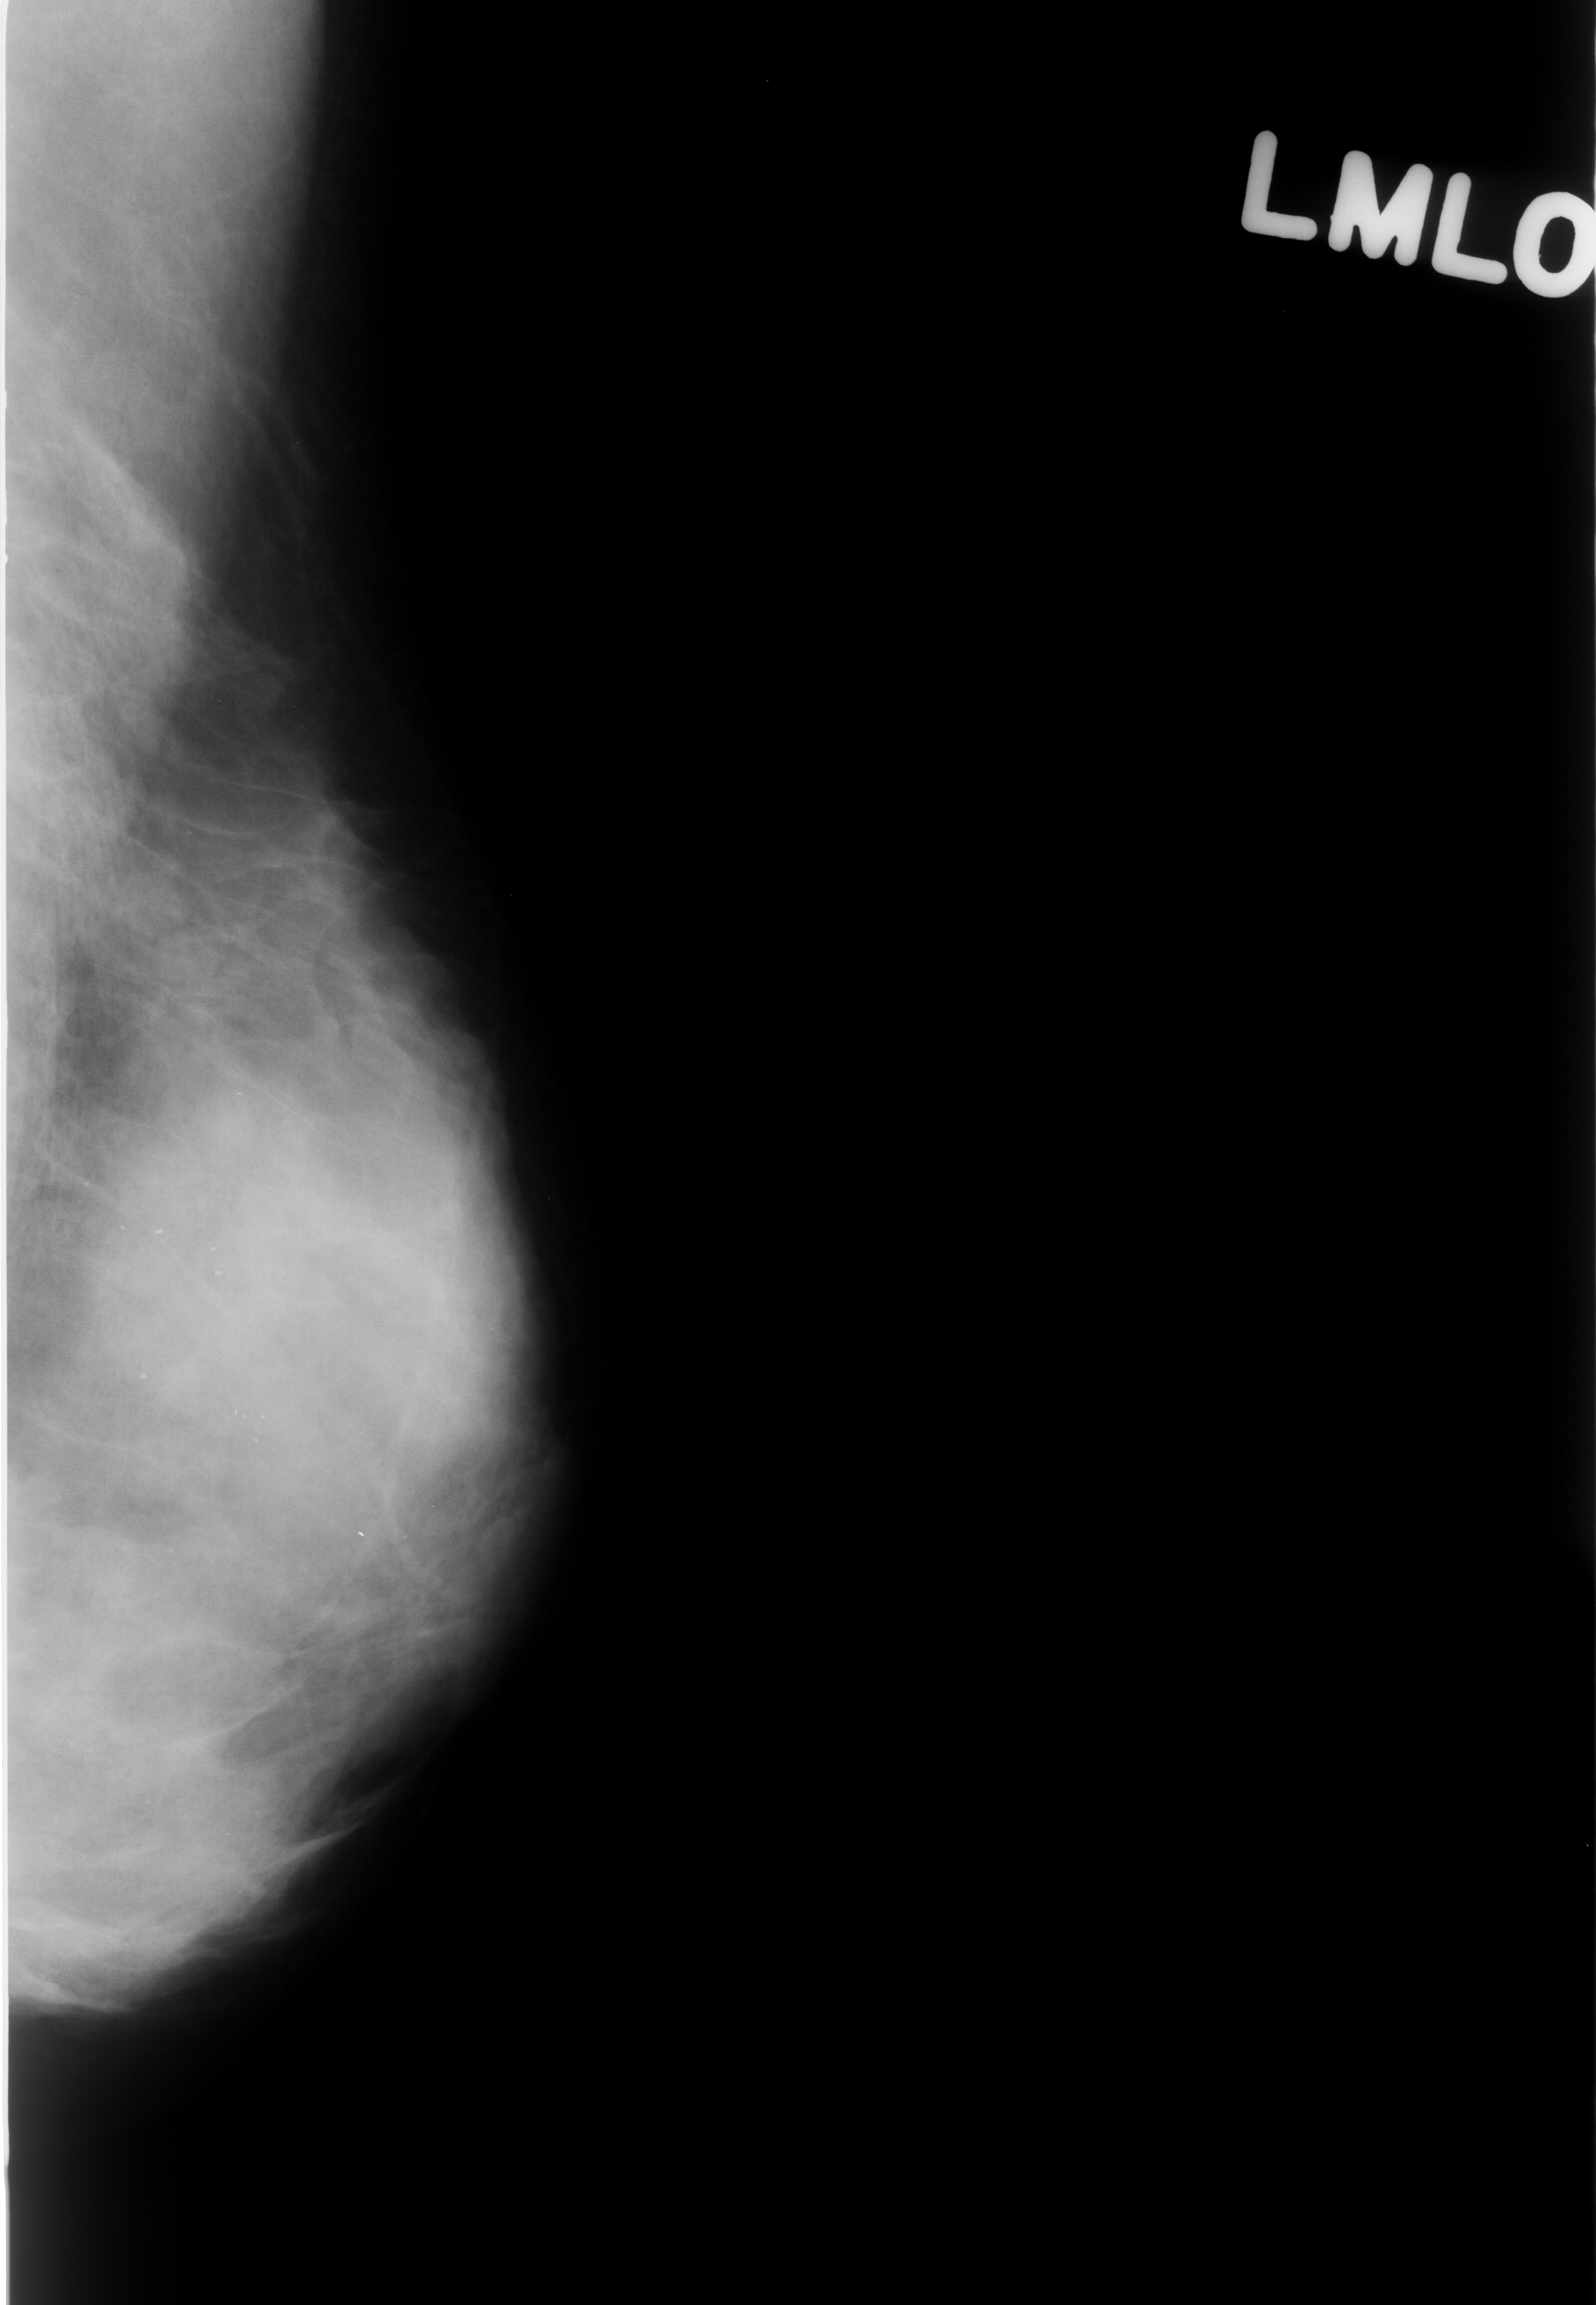
Scanned film-screen mammogram; left breast; mediolateral oblique (MLO) view; breast composition: extremely dense (BI-RADS density category 4 of 4).
Marked abnormality: calcifications, morphology punctate, distribution diffusely scattered; BI-RADS assessment category 2; subtlety rating 4 on a 1 (subtle) to 5 (obvious) scale; pathology result (as recorded, not read from the image): benign.